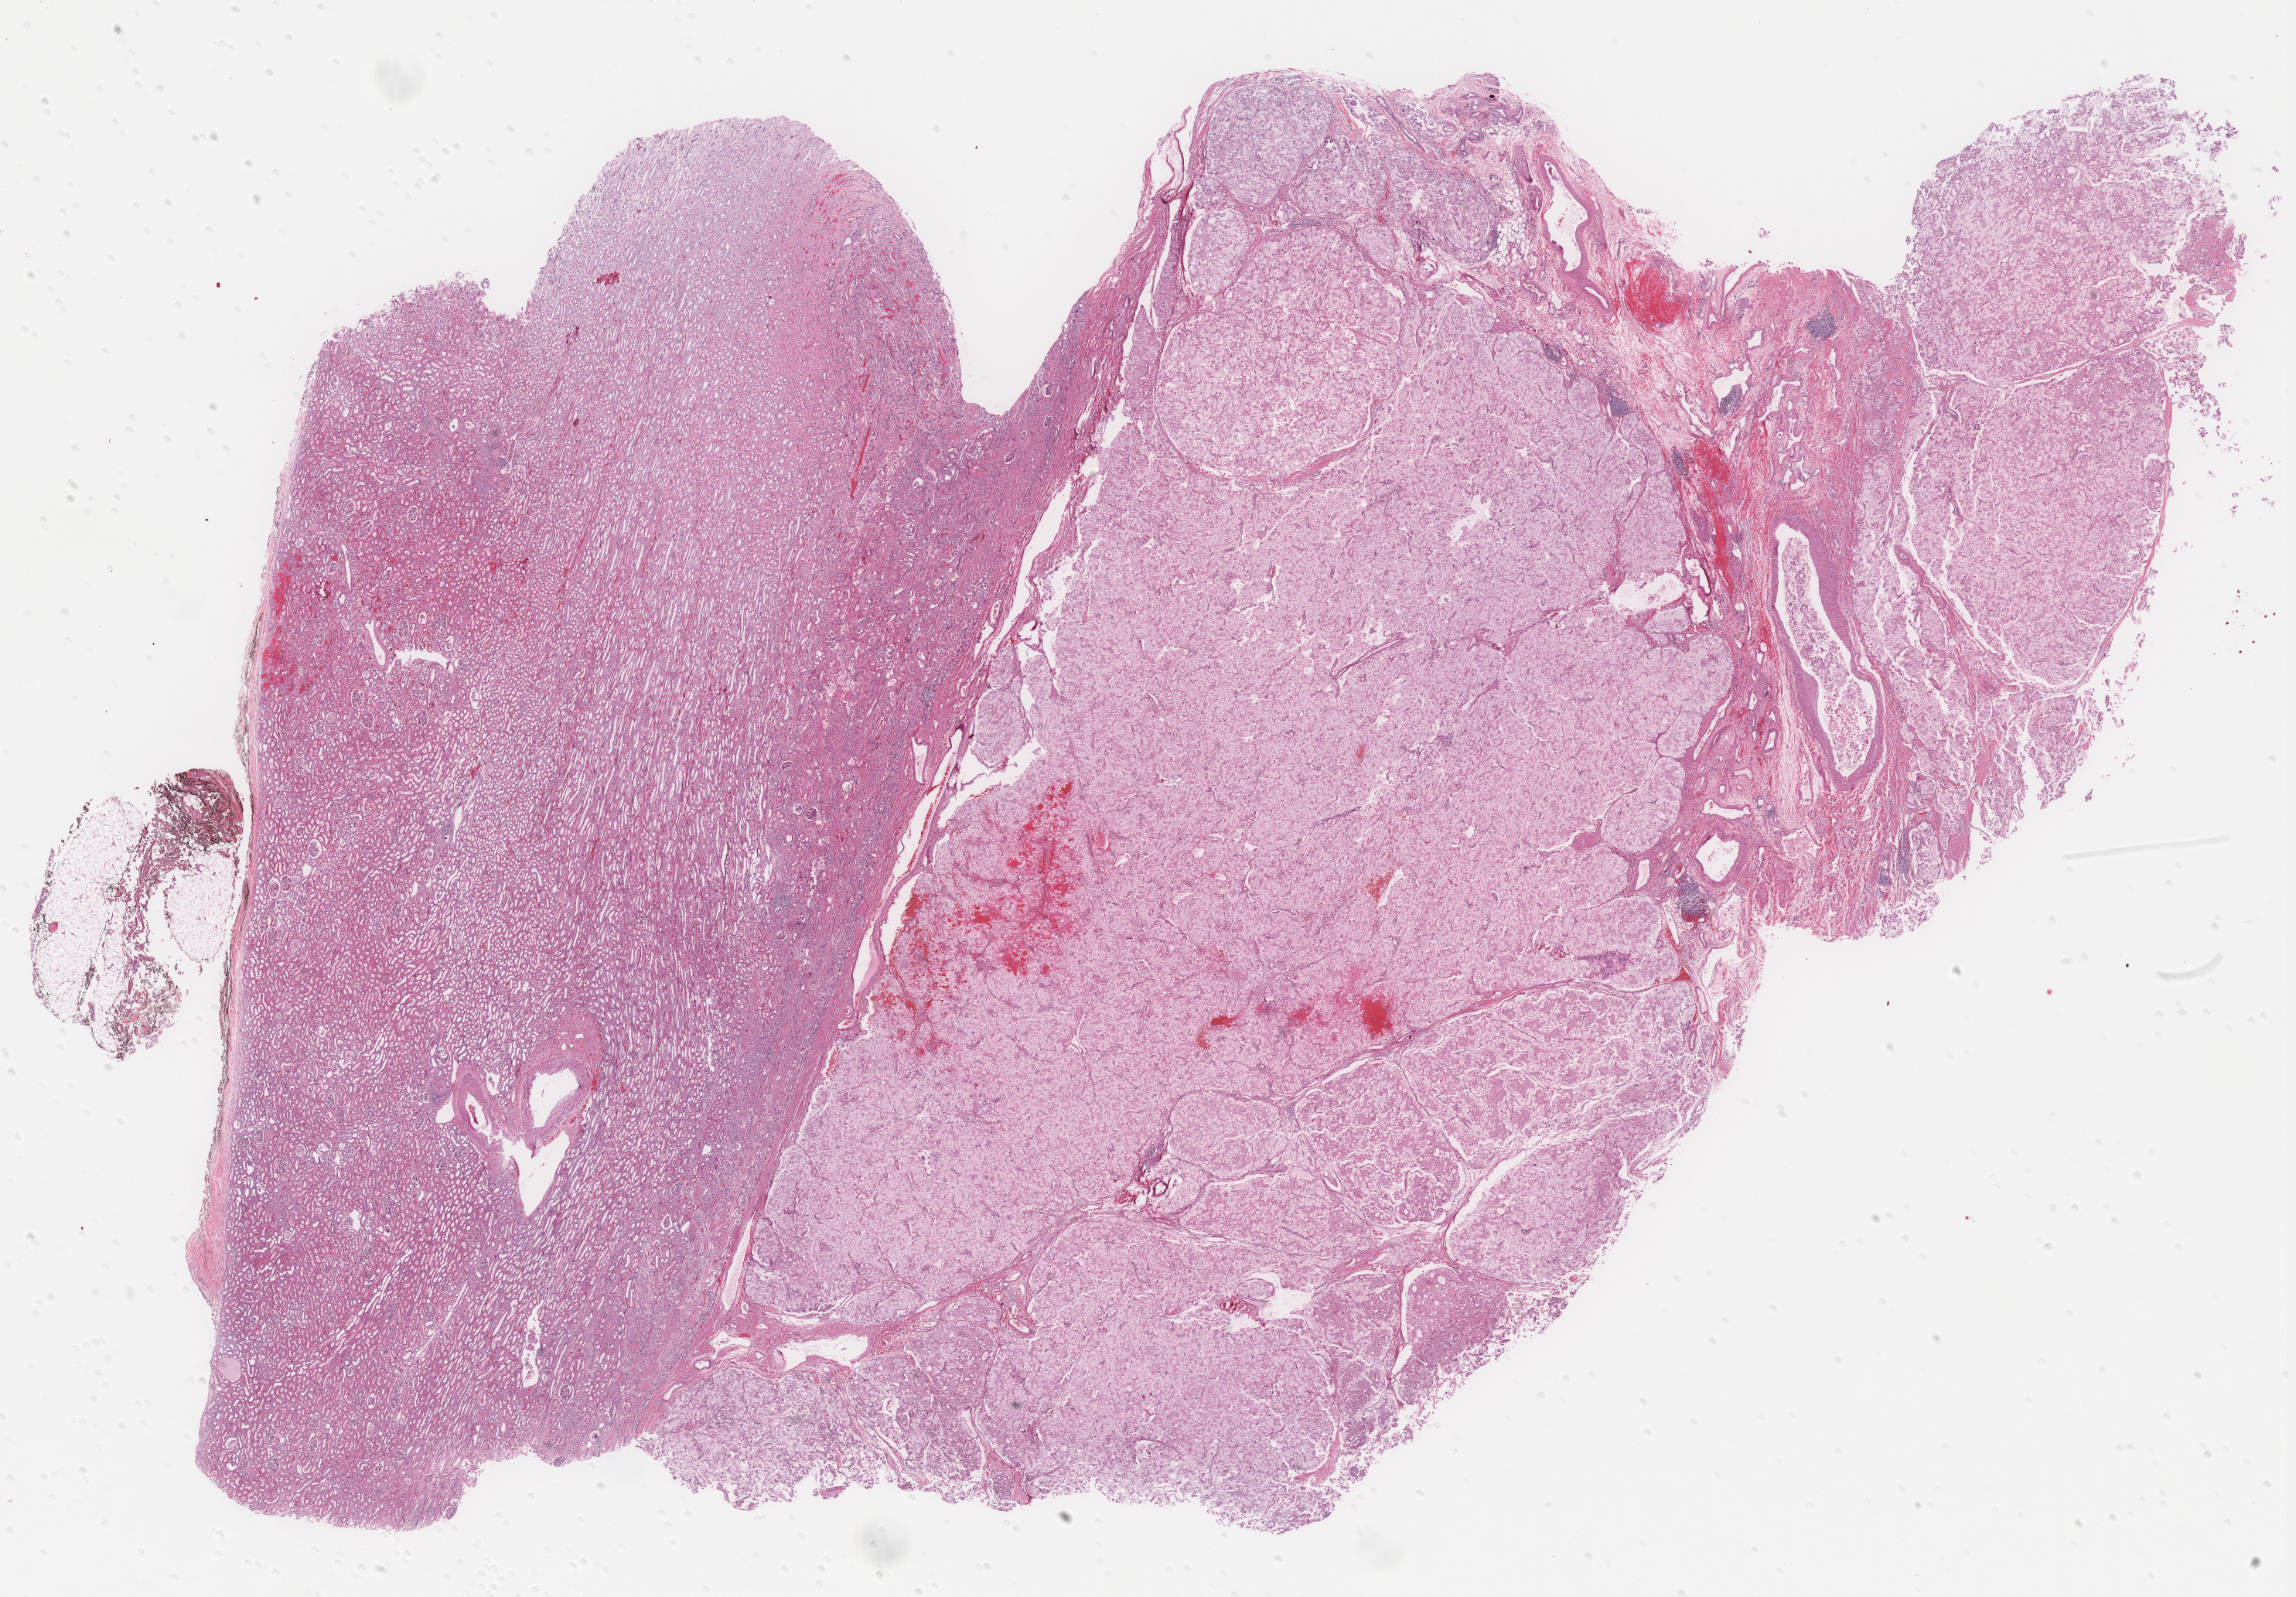
Digitized Hematoxylin and eosin (H&E) stained tissue section (whole slide), a low-resolution overview of the entire scanned area, about 23.7 x 16.5 mm, formalin-fixed paraffin-embedded (FFPE) diagnostic section, kidney, primary tumour sample. Patient: female, age at initial diagnosis 48 years.
- AJCC pathologic stage: II (6th edition)
- diagnosis: Renal cell carcinoma, chromophobe type
- laterality: right